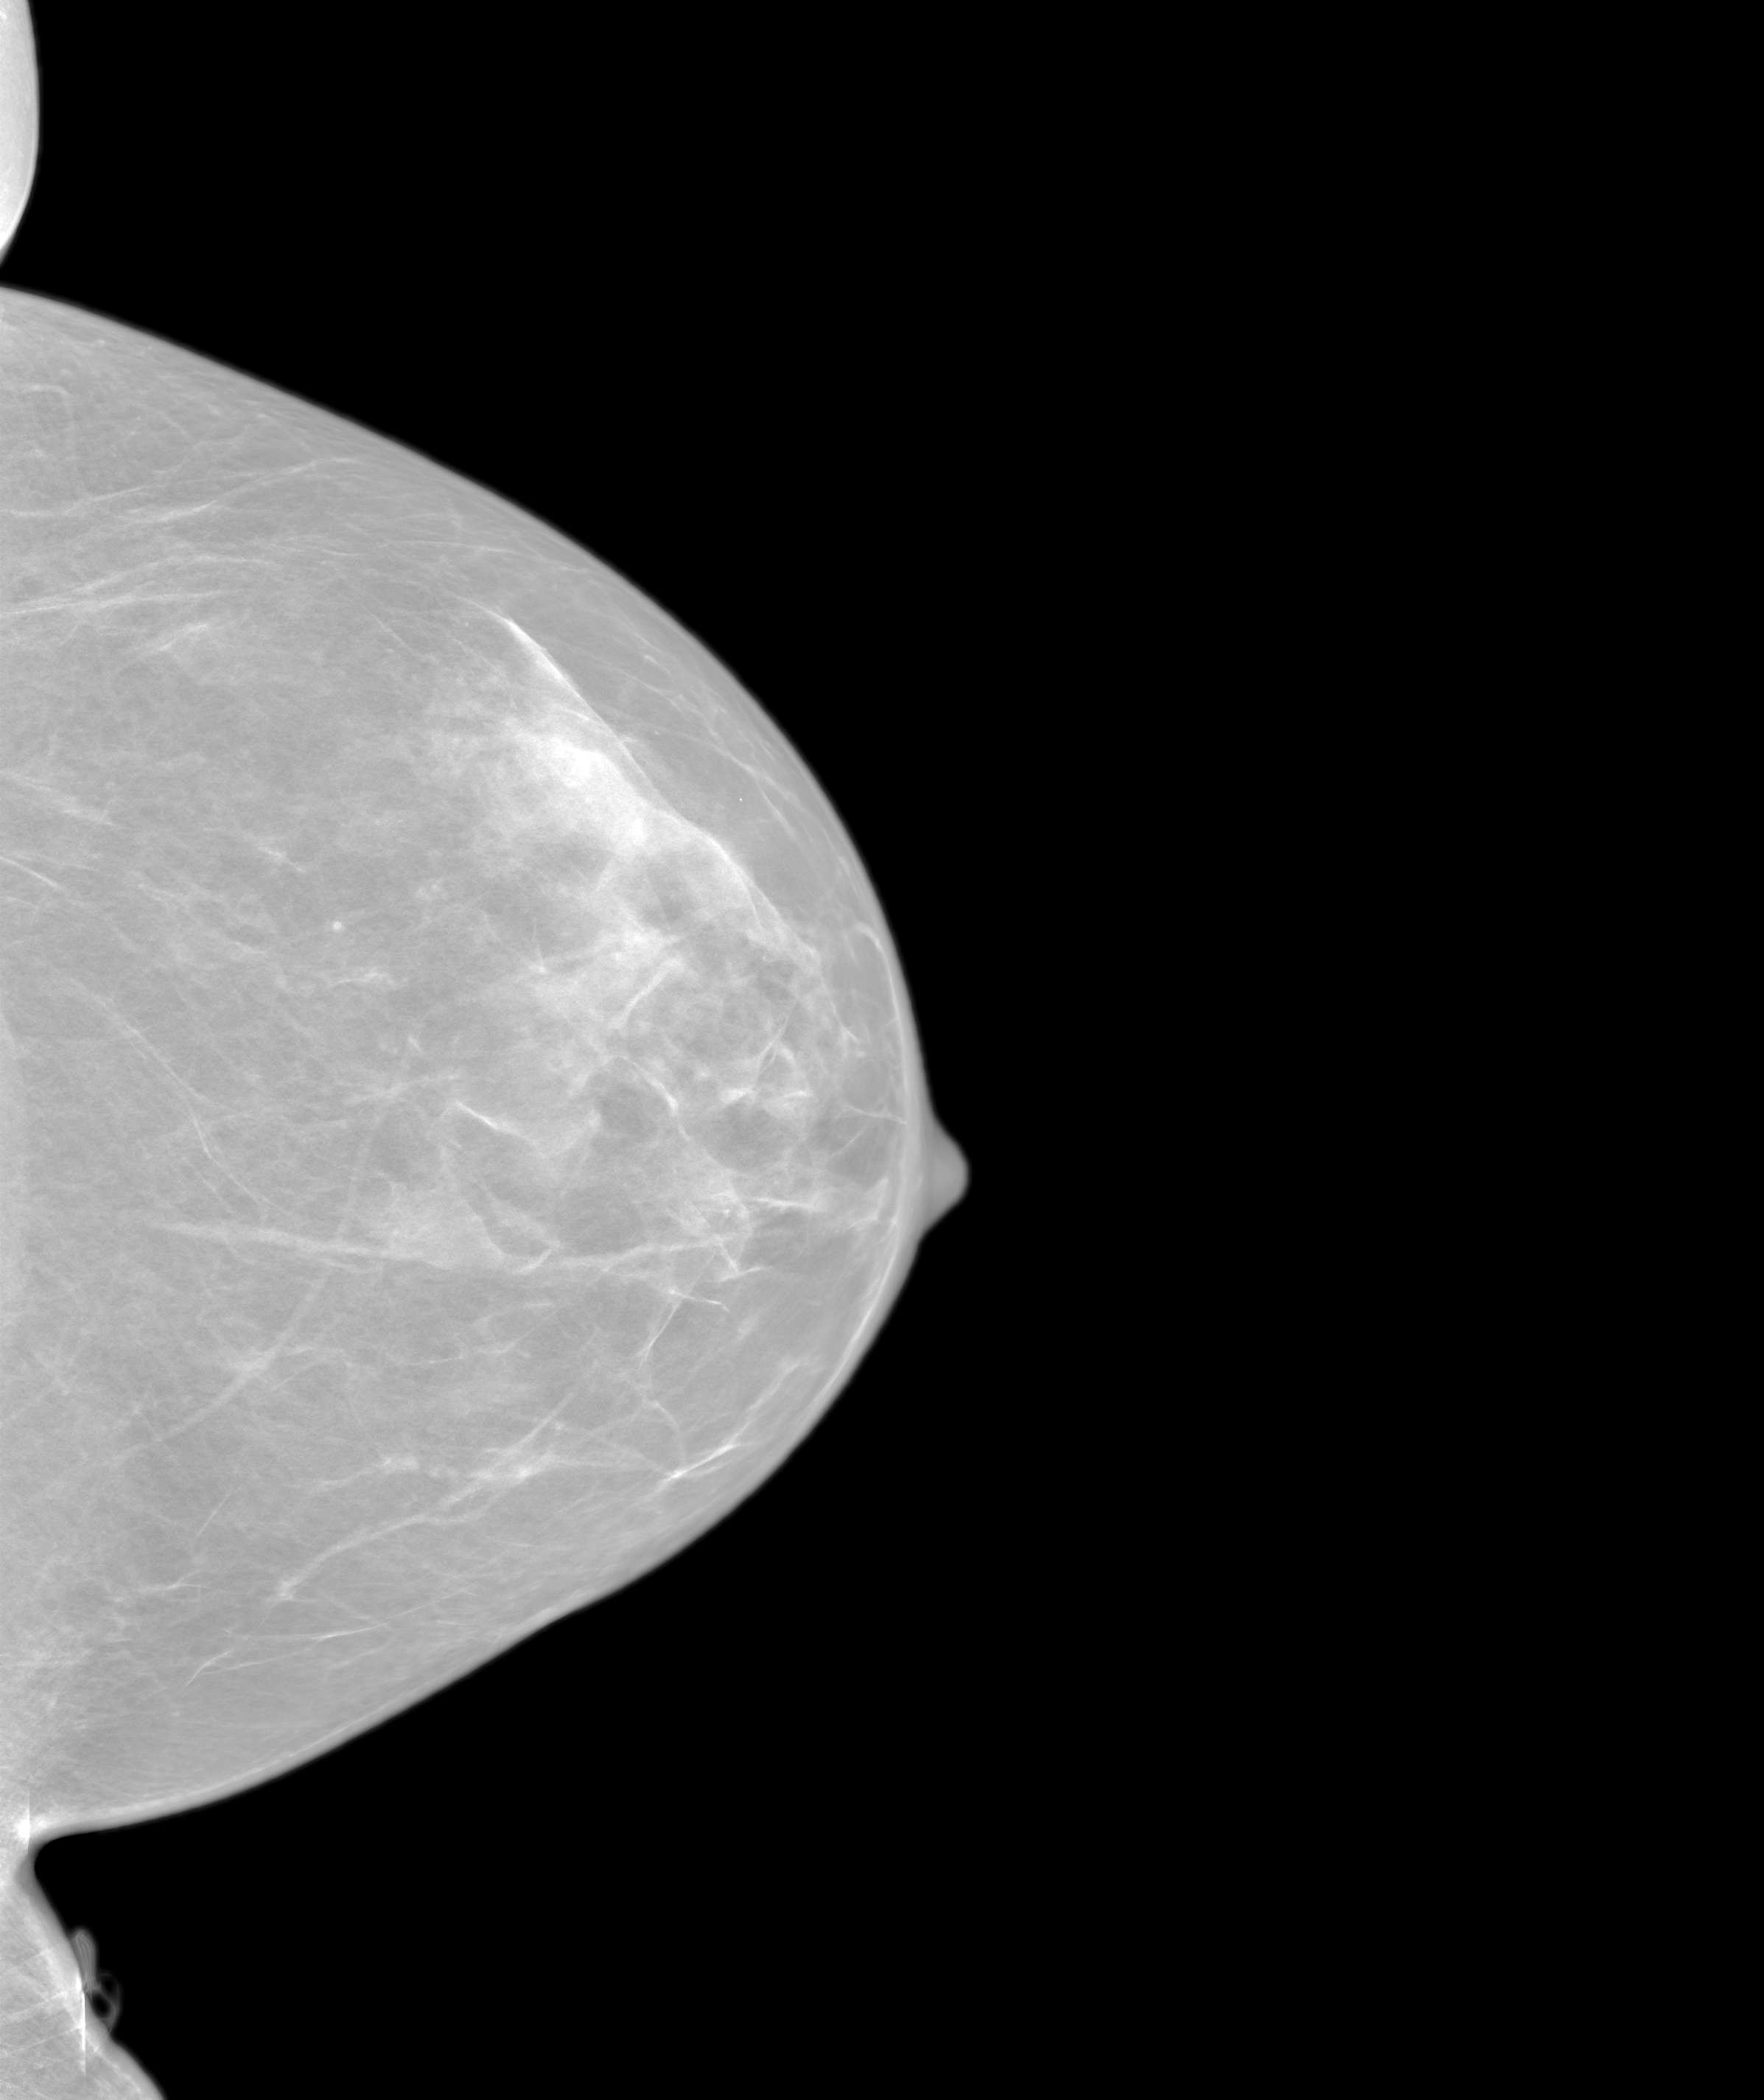
Screening examination, system: SenoIris_1SP2(440). Patient aged 49 years (female).
Image type: synthesized 2-D view from tomosynthesis. Breast: left. Projection: CC view.